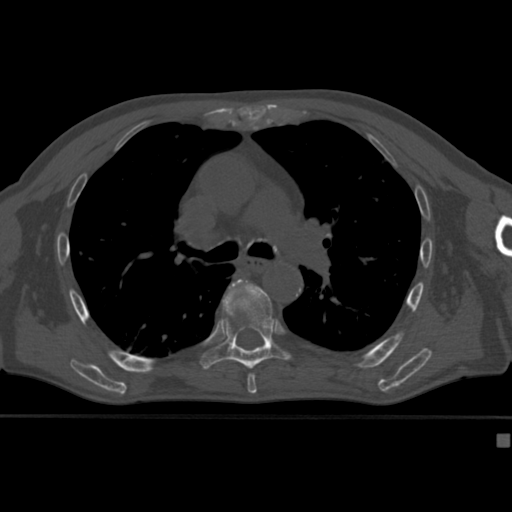
CT including the spine, one axial slice. Position 283 of 430 along the scan axis. Reconstruction kernel Br40s. 120 kVp. Bone window (W 1800 / L 400 HU). 1.5 mm slice thickness. 512 × 512 image matrix, field of view 337 × 337 mm. Patient: male, 64 years. From the clinical record (not read from this slice): primary cancer: uterus.
Structures marked on this image (semi-automatic segmentation, software-assisted and operator-edited):
- T6 vertebra: box from (x=231, y=280) to (x=256, y=382) px
- T7 vertebra: (x=201, y=280)–(x=291, y=372)